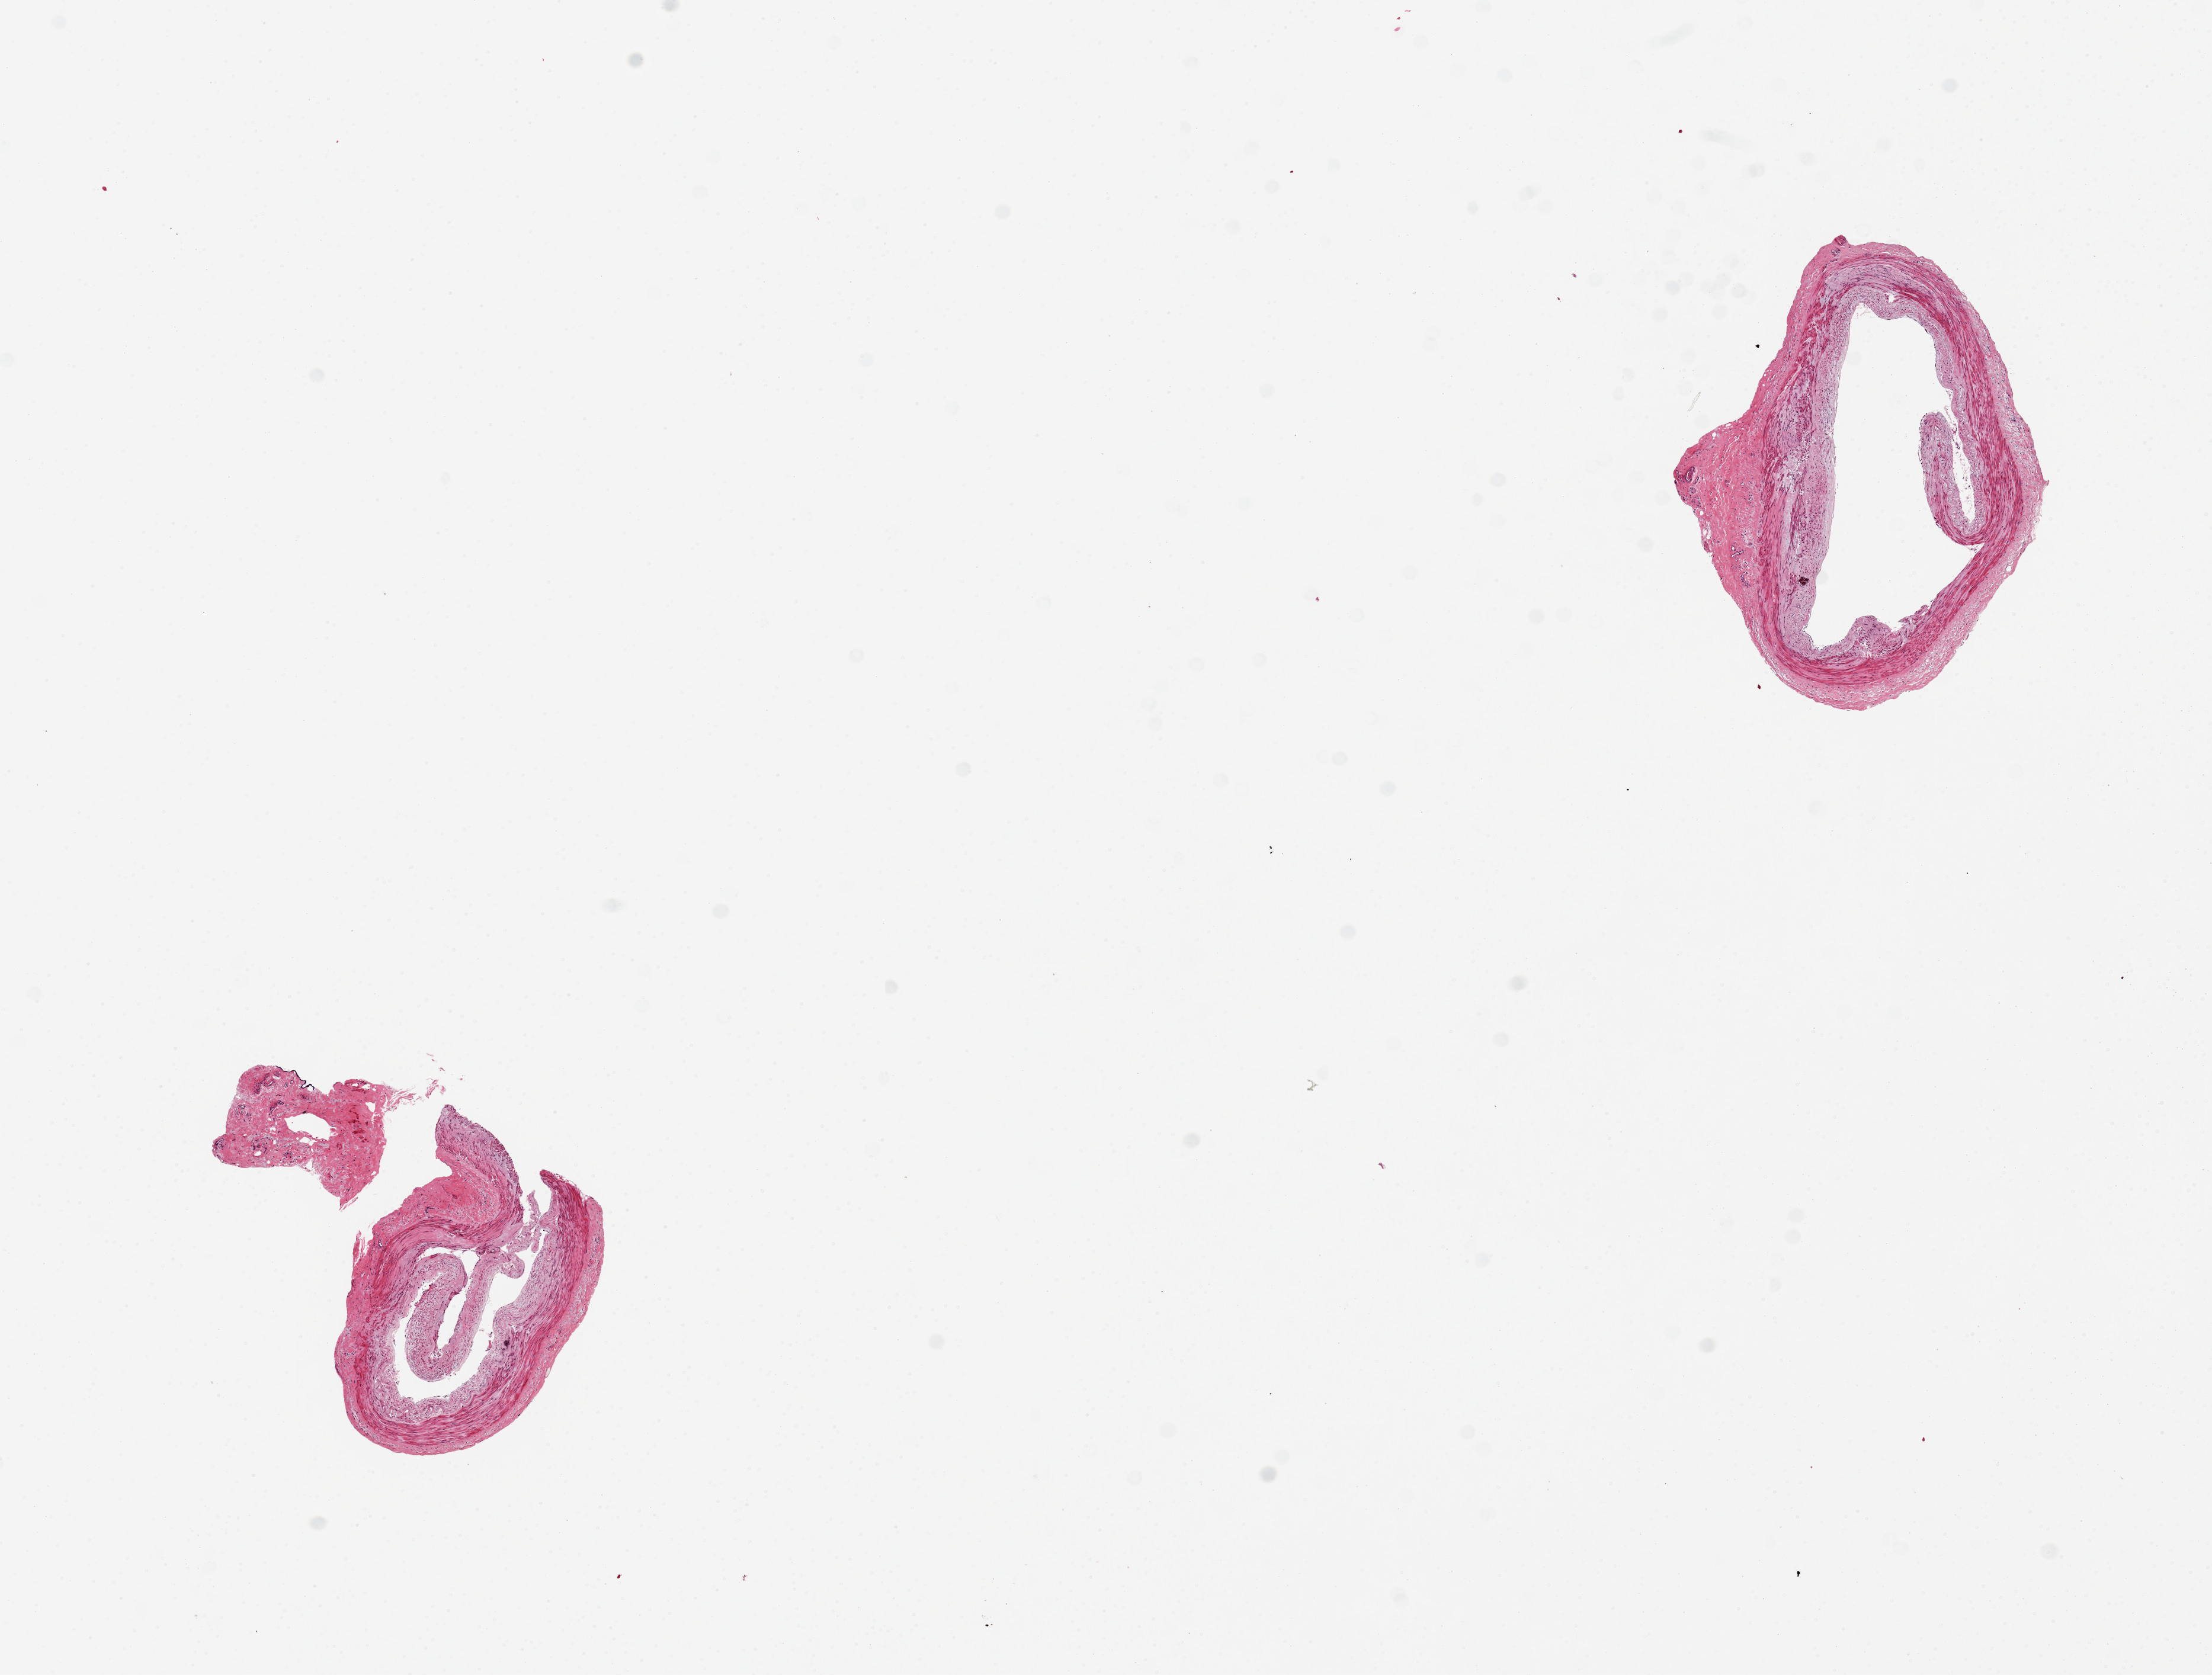
Whole-slide image, H&E stain, shown as a low-resolution overview of the whole scanned area (about 14.8 x 11.2 mm, from a 20x scan); PAXgene-fixed, paraffin-embedded tissue; section of tibial artery (target tissue); tissue donor sample. Donor sex: male.
Reviewer comment on this tissue sample: 2 pieces (2x1.5 and 3x2.5mm), artery, one separate minute frament of contaminant fibrous tissue; One arery aliquot has small nubbin of fibrous tissue ~0.5mm.